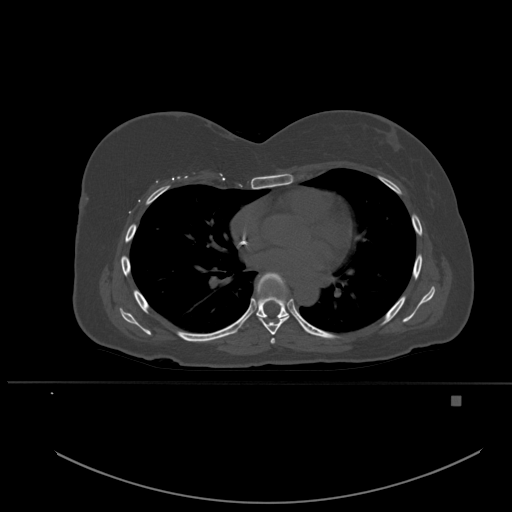
CT including the spine, one axial slice; position 343 of 651 along the scan axis; bone window (W 1800 / L 400 HU); 1.5 mm slice thickness; 512 × 512 image matrix, field of view 443 × 443 mm. Patient: female, 49 years. From the clinical record (not read from this slice): primary cancer: breast.
Outlined on this slice (semi-automatic segmentation, software-assisted and operator-edited):
- T5 vertebra: bounding box [x1, y1, x2, y2] px = [270, 338, 275, 344]
- T6 vertebra: [259, 315, 290, 335]
- T7 vertebra: [247, 272, 289, 326]